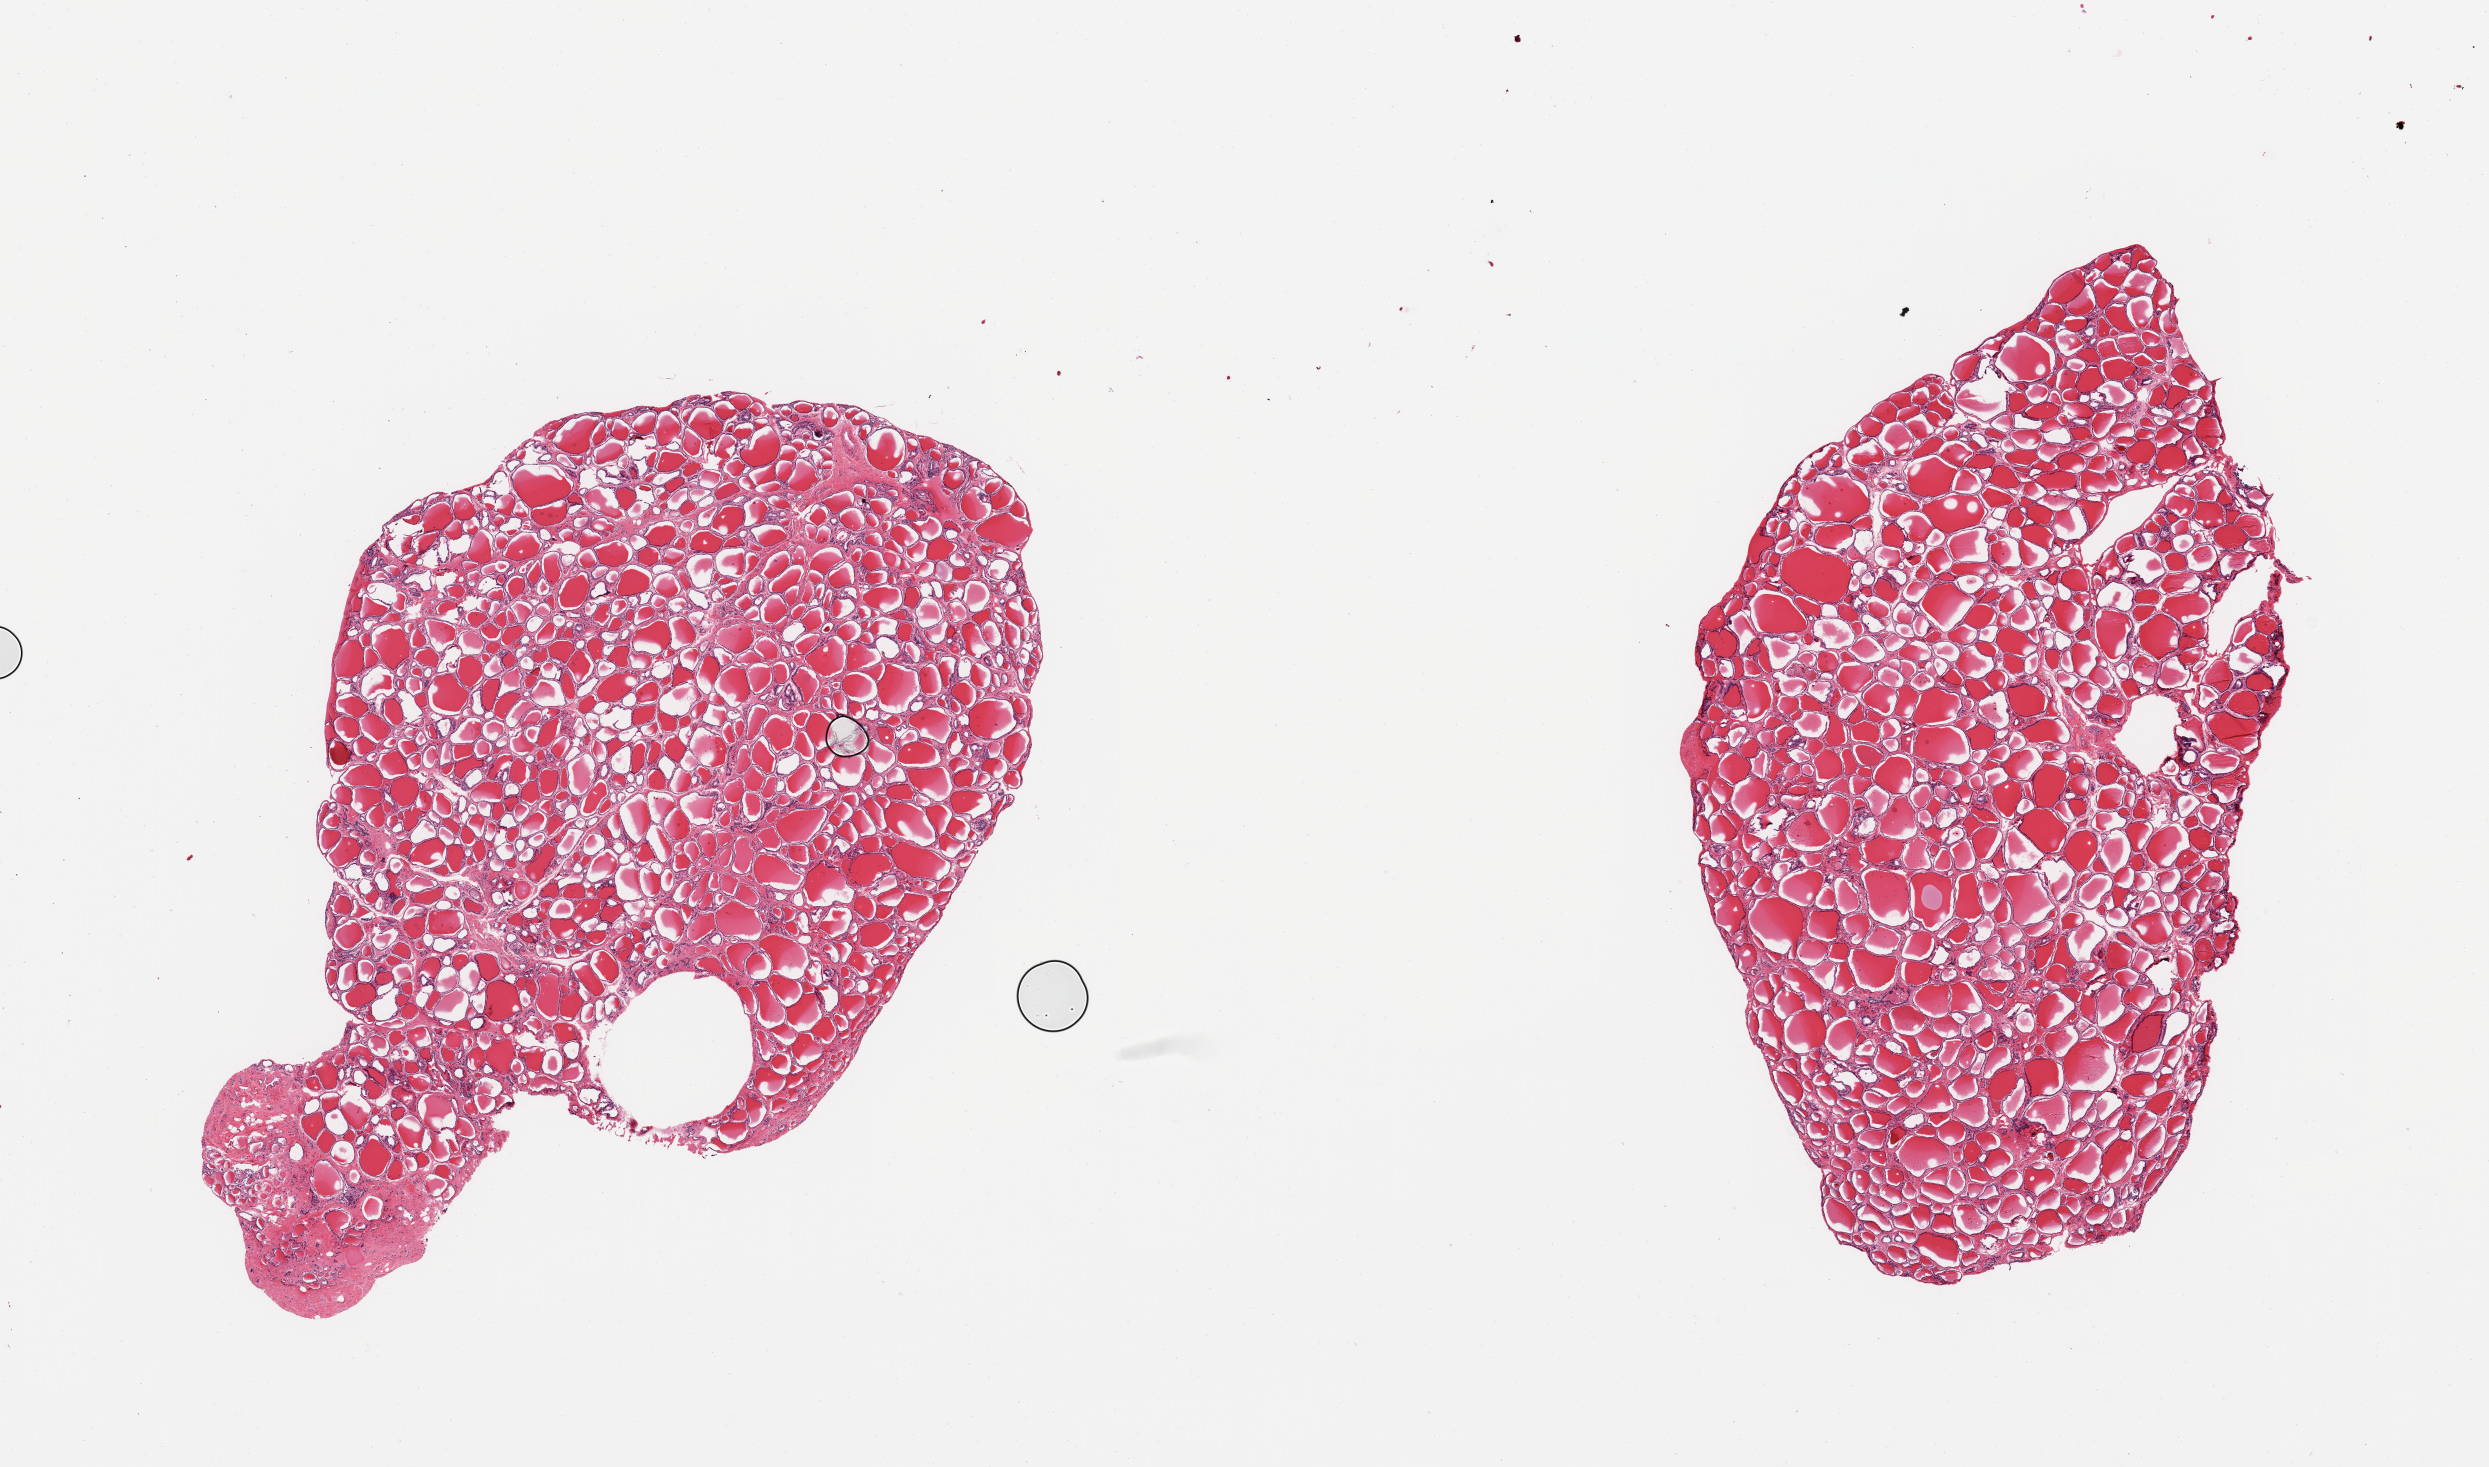
Whole-slide image, haematoxylin and eosin stain, brightfield — a low-resolution overview of the entire scanned area, about 19.7 x 11.6 mm (slide scanned at 20x), PAXgene-fixed, paraffin-embedded tissue, sampled site (target tissue): thyroid, donor tissue sample. Donor sex: male.
* reviewer comment on this tissue sample: 2 pieces